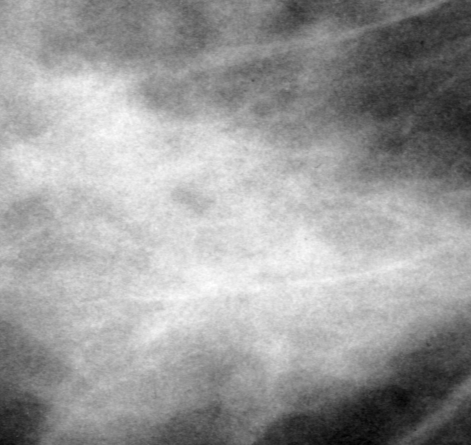
Cropped region of a digitized screen-film mammogram centred on a radiologist-marked abnormality, right breast, MLO view, BI-RADS breast density category 2 (scale 1–4).
Marked abnormality: mass, shape irregular, margins ill defined; BI-RADS assessment category 3; pathology result (as recorded, not read from the image): malignant.